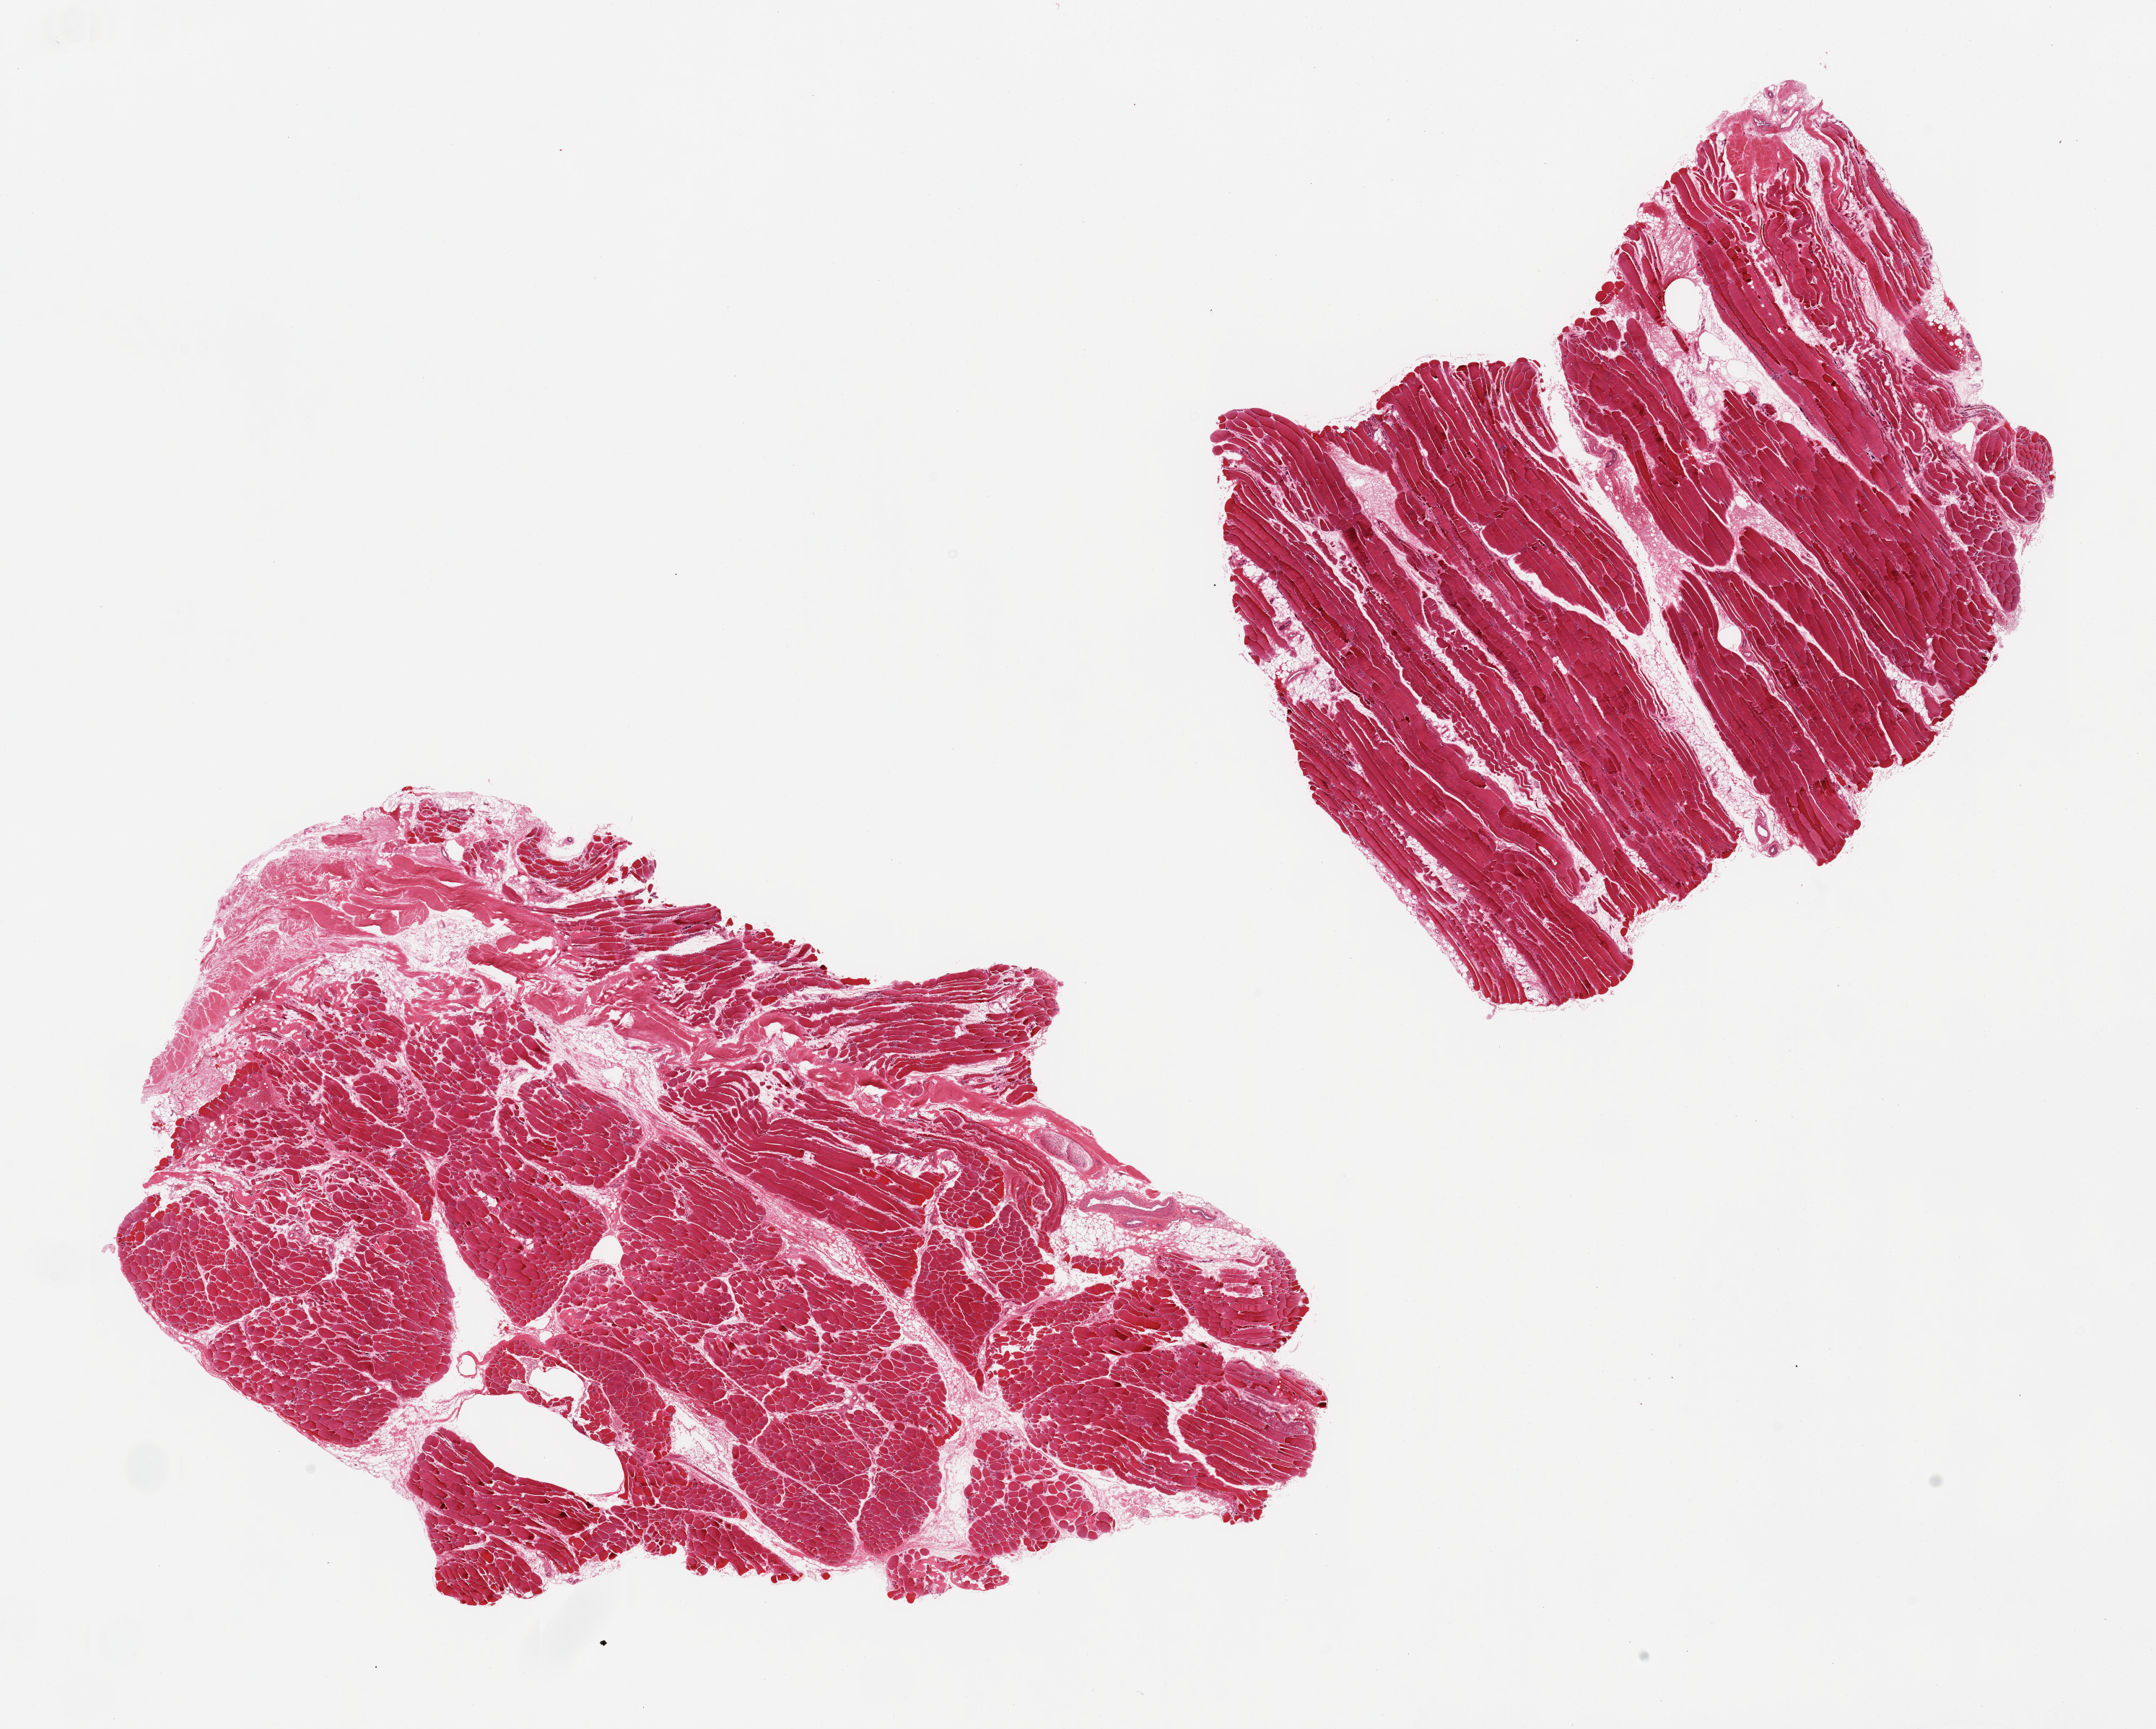
Haematoxylin and eosin whole-slide image — whole scanned area (about 23.6 x 18.9 mm, from a 20x scan) shown as a low-resolution overview, PAXgene-fixed, paraffin-embedded tissue, target tissue: skeletal muscle, donor tissue sample. Donor sex: female.
Review note (as recorded): 2 pieces, ~15% interstitial fat.